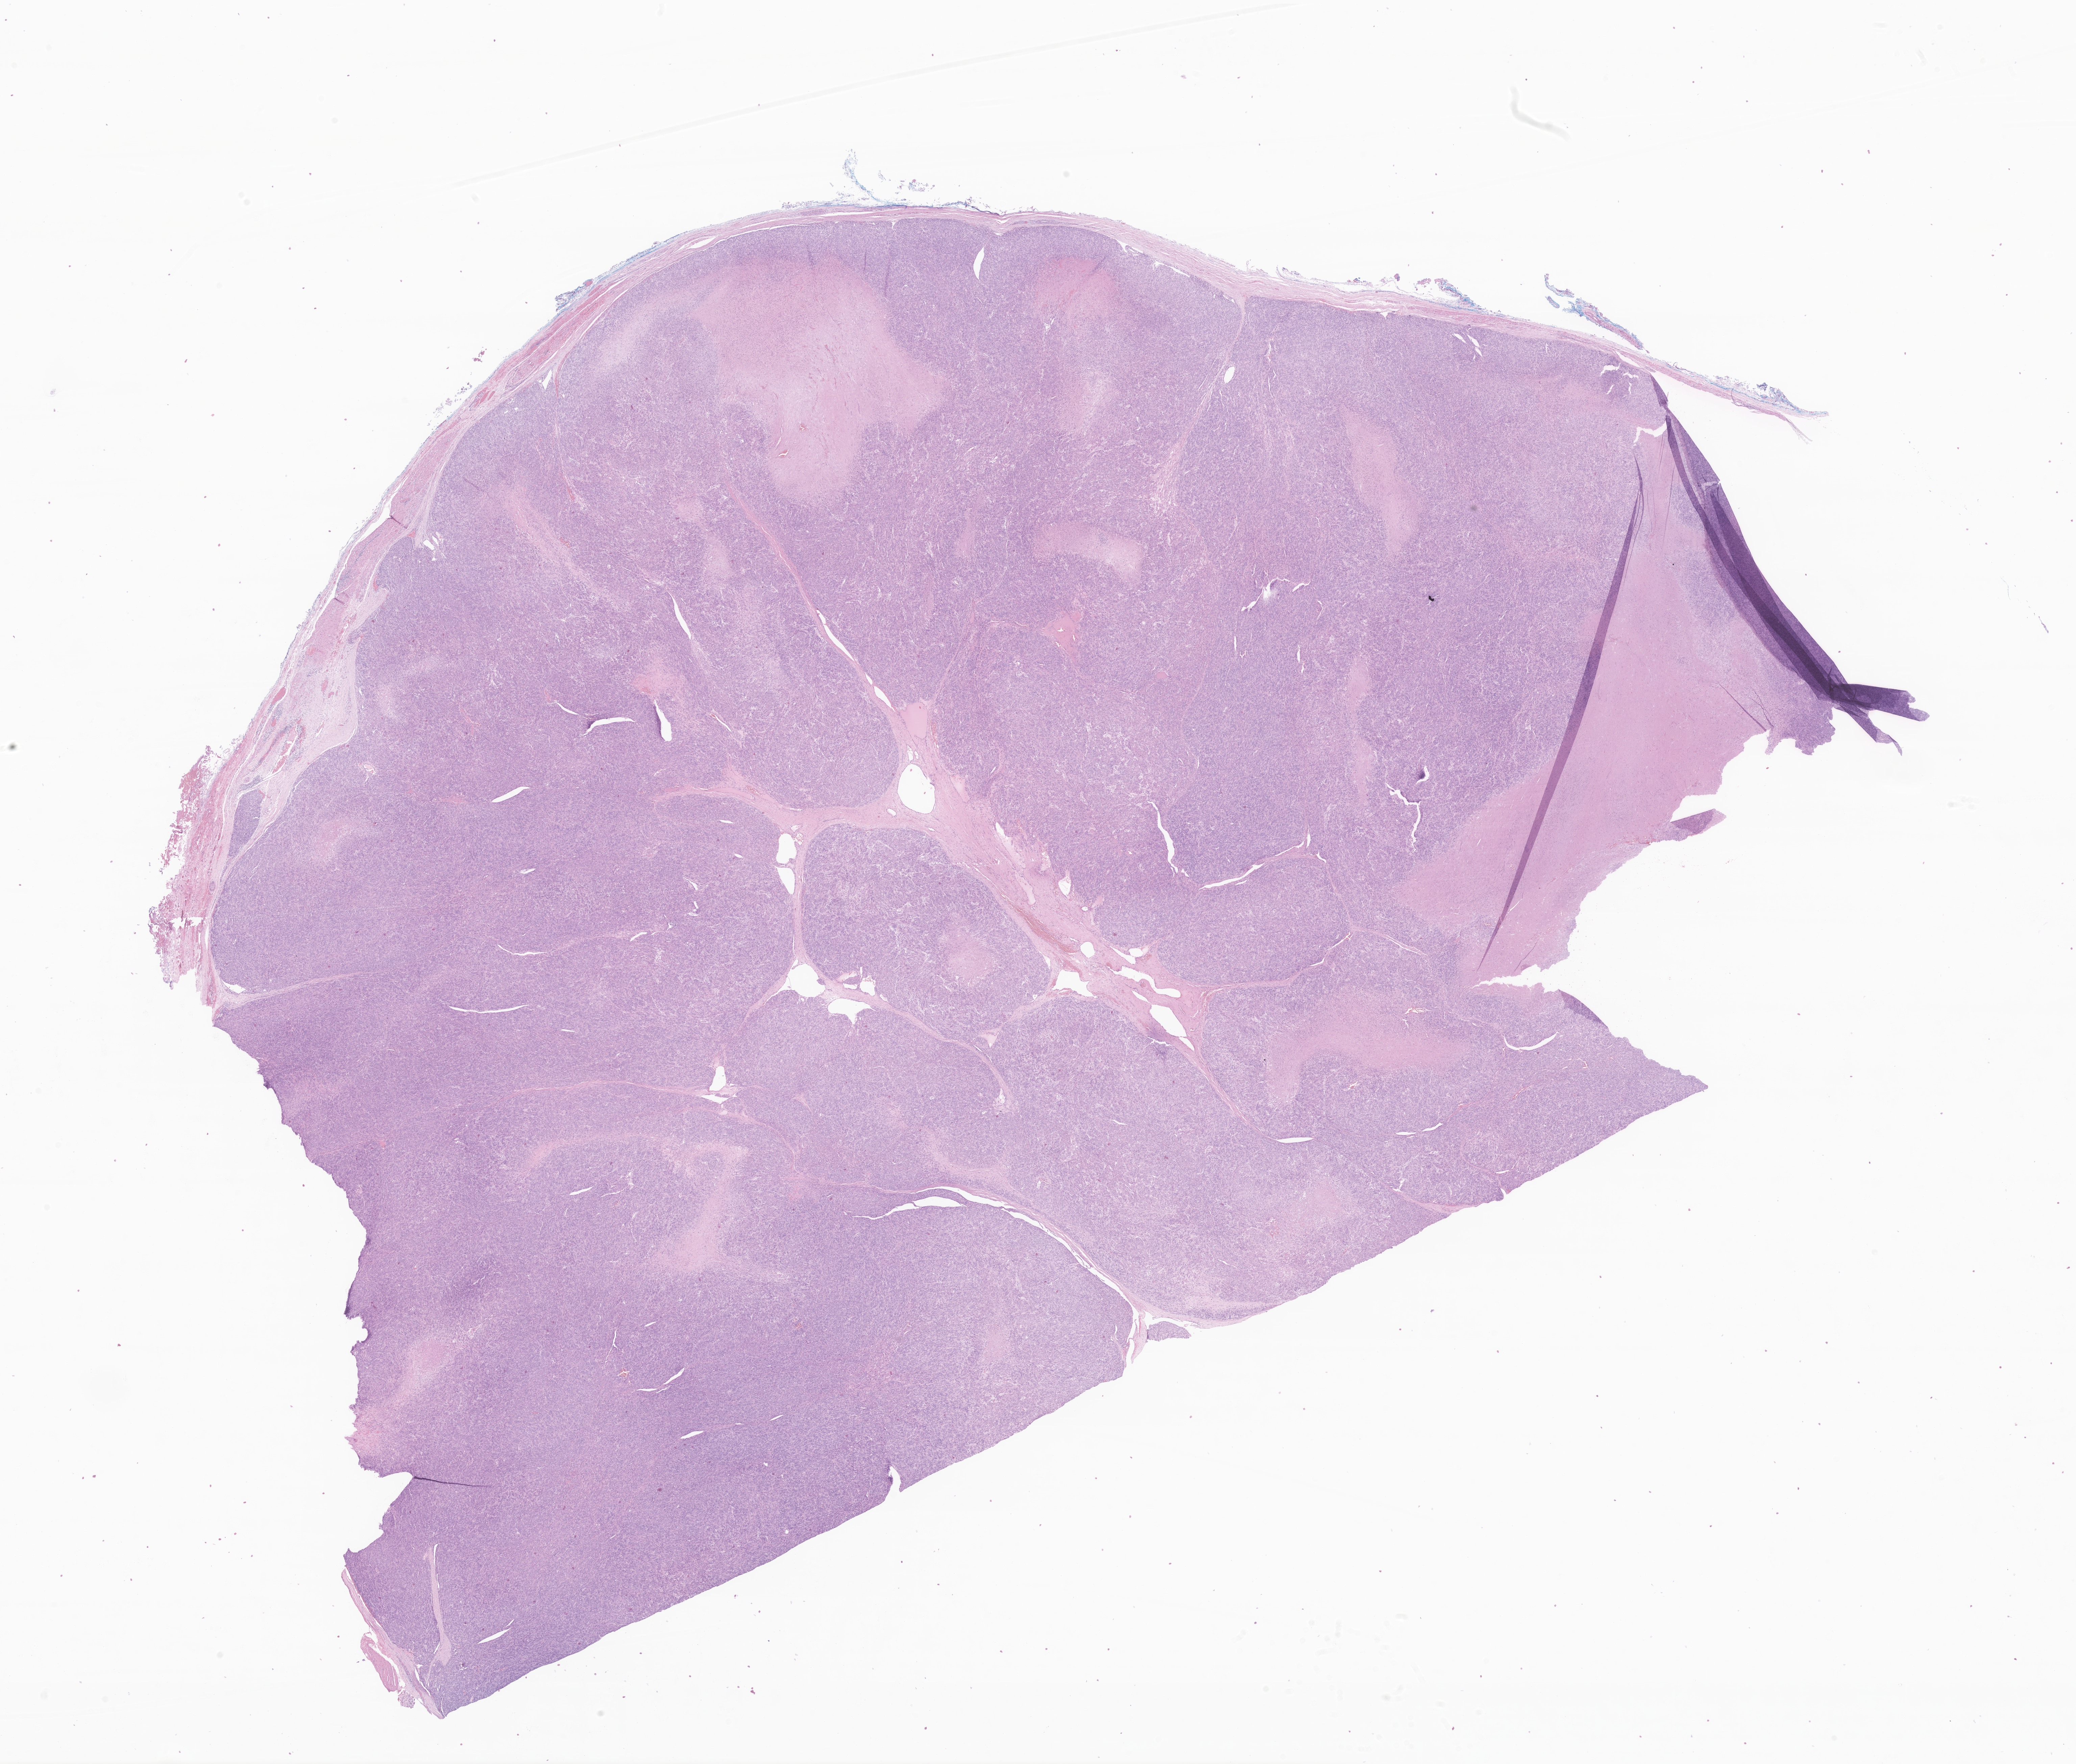
Hematoxylin and eosin (H&E) whole-slide image of tumor tissue from the soft tissues of head and neck — a low-resolution overview of the entire scanned area, about 25.9 x 22.0 mm. Formalin-fixed paraffin-embedded section. Patient: male, age 170 months (14 years 2 months).
Diagnosis (ICD-O-3 morphology term): Leiomyosarcoma, NOS.